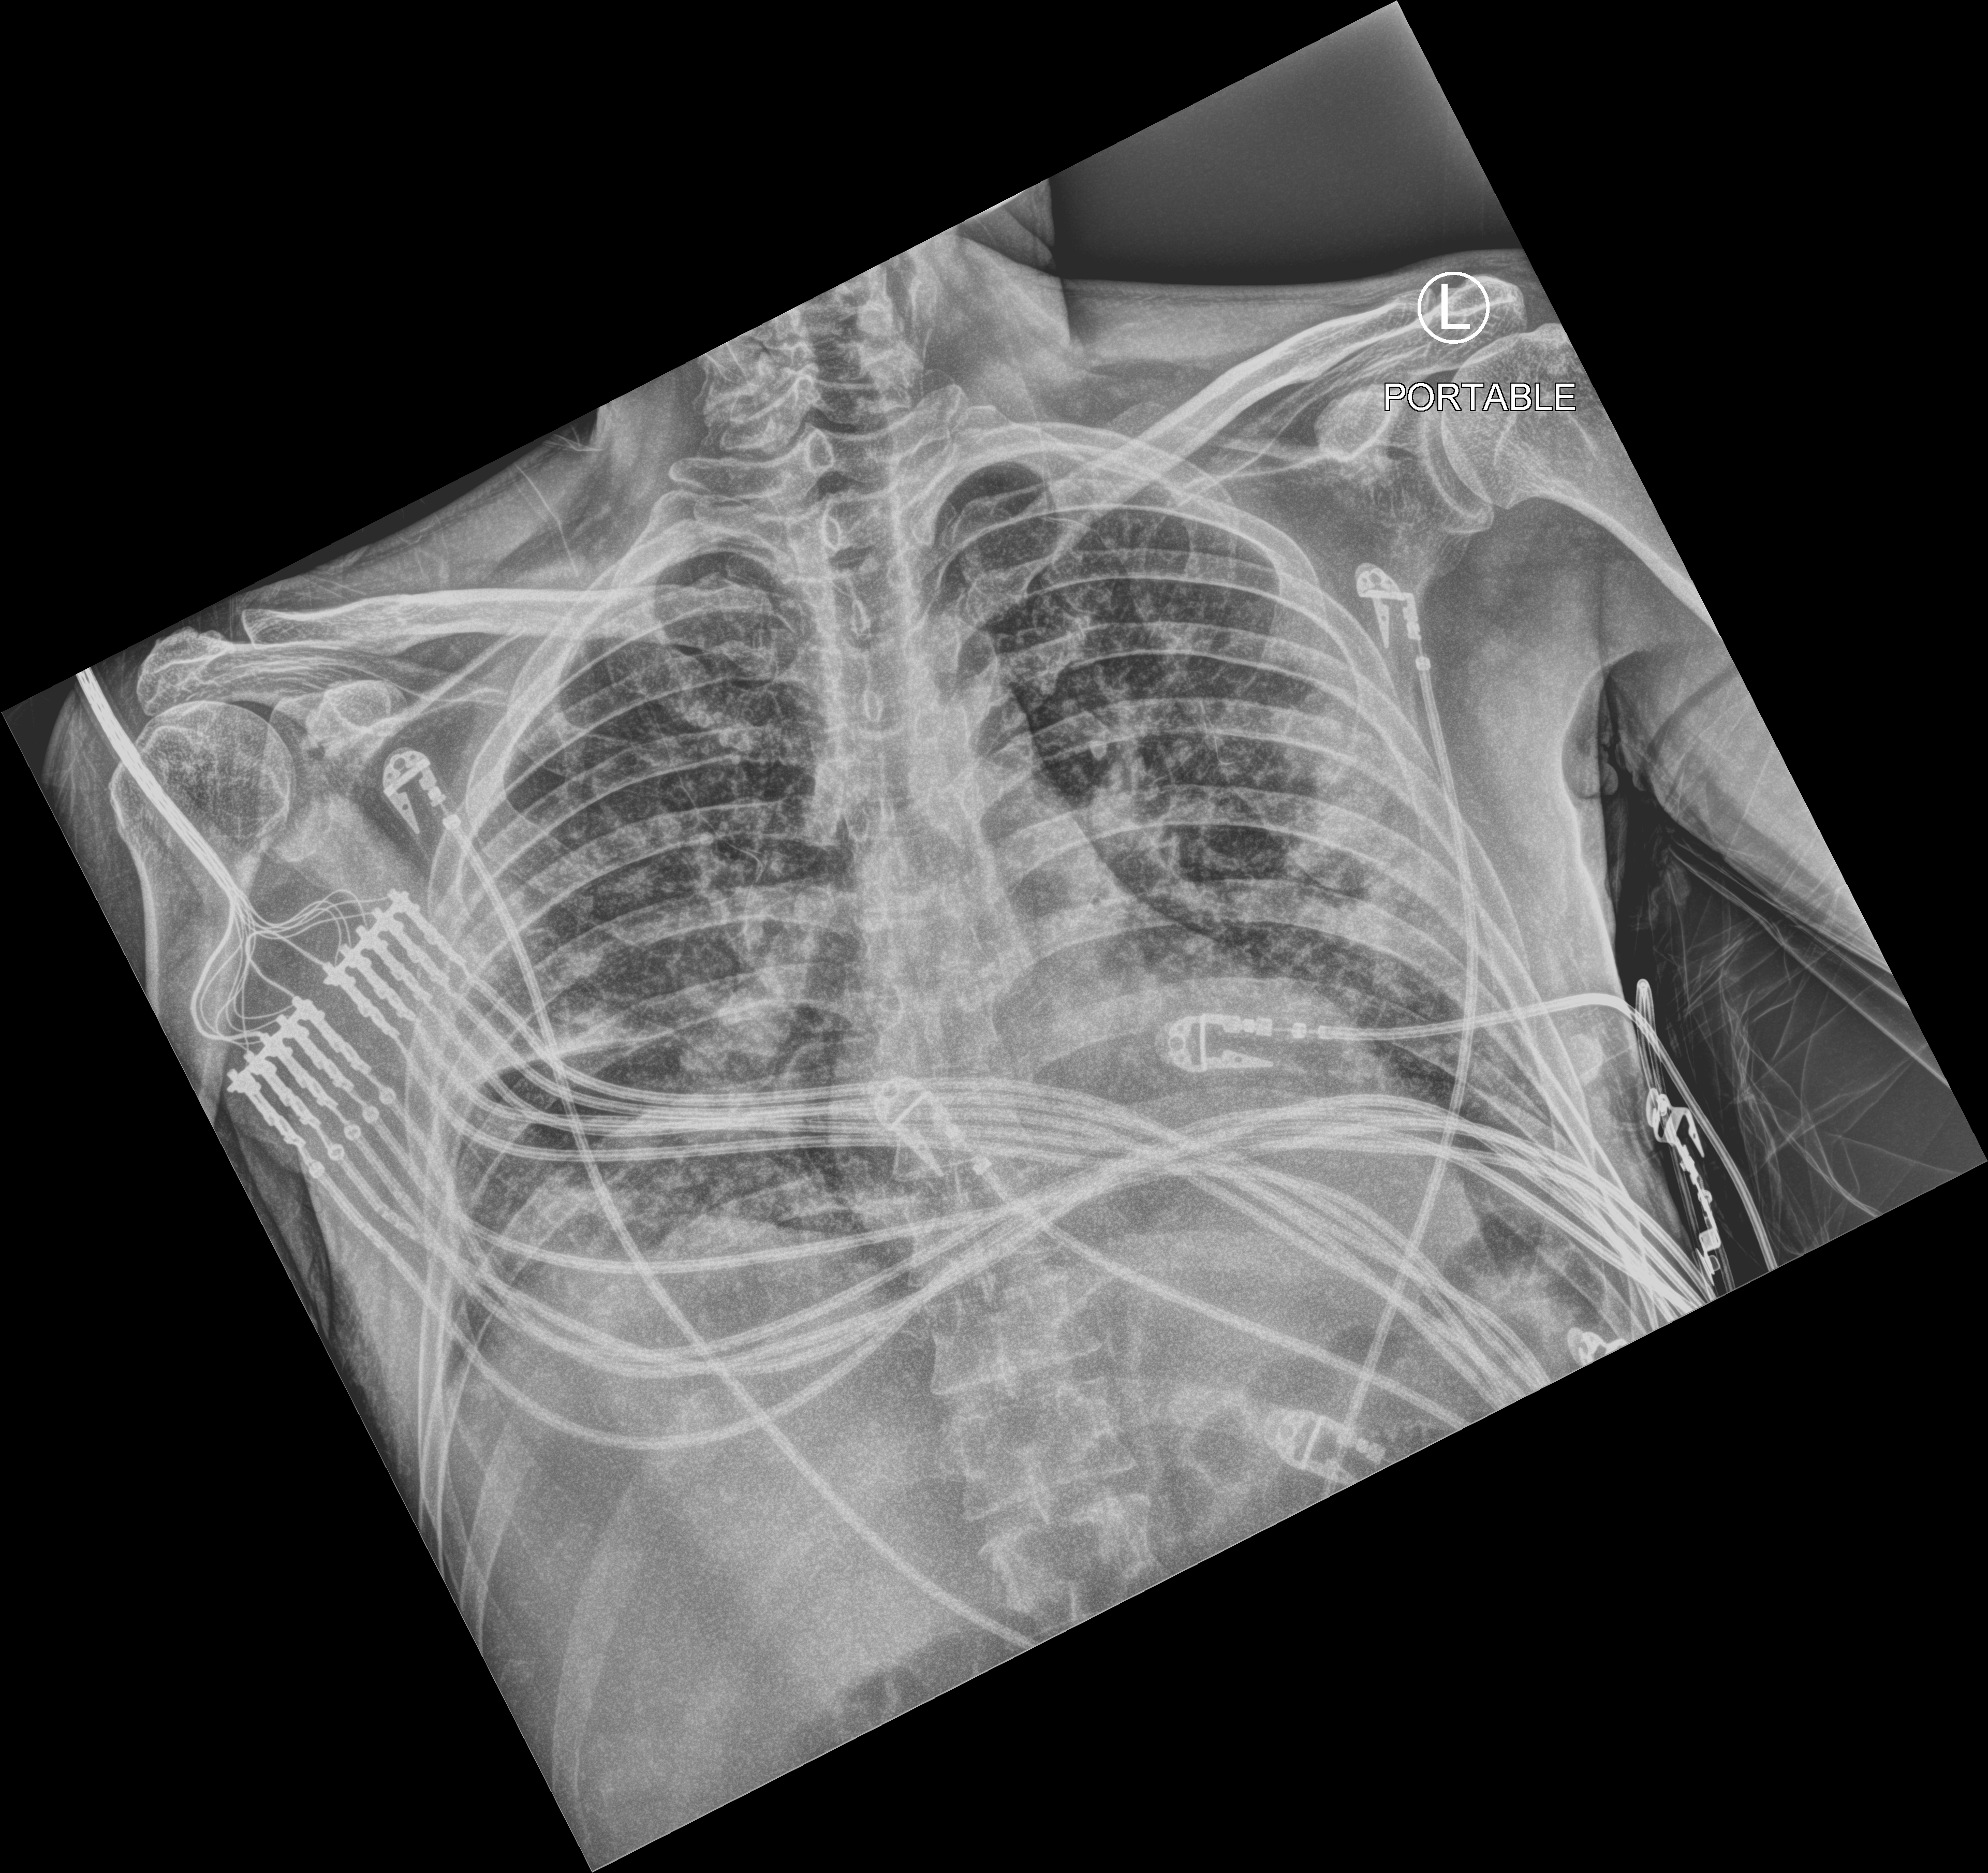
Bedside chest radiograph (computed radiography). Male patient hospitalised with COVID-19, age 18–59 years.
From the hospital-stay record, not from the radiograph (when in the stay this image was taken is not recorded): diabetes (admission record): yes.